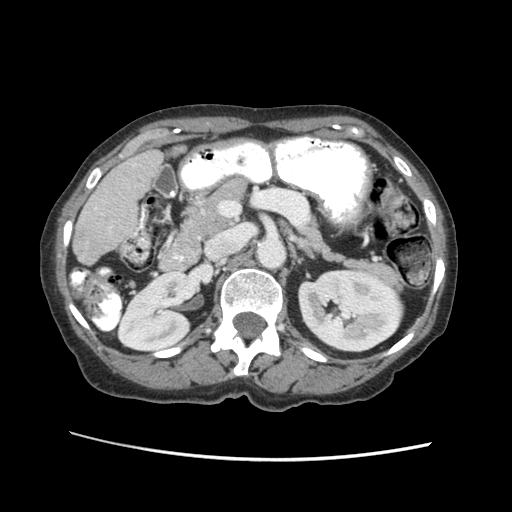
Contrast-enhanced abdominal CT (liver protocol), one axial slice. Position 18 of 63 along the scan axis. 120 kVp. Soft-tissue window (W 400 / L 40 HU). 2.5 mm slice thickness. 512 × 512 image matrix. Case-level facts recorded for this patient, not image findings: diagnosis: hepatocellular carcinoma (patient treated with transarterial chemoembolisation; whether this scan precedes or follows treatment is not stated here); TNM stage (as recorded): Stage-I; Child-Pugh class: B.
Annotated regions visible in this slice (semi-automatically segmented with operator editing):
- liver parenchyma outside the tumour (the mass and vessels are separate outlines, so this box may not span the whole liver): bounding box (x1, y1, x2, y2) in pixels: (72, 148, 162, 264)
- liver vessels: (93, 206, 95, 208)